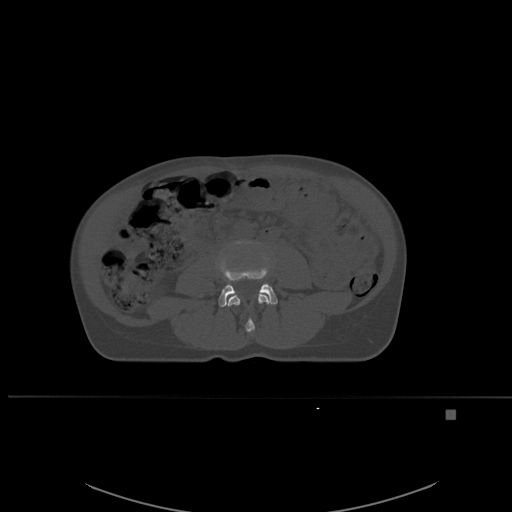
CT including the spine, one axial slice; slice 201 of 537 in the series (ordered by position); bone window (W 1800 / L 400 HU); 1.5 mm slice thickness; 512 × 512 image matrix. Female patient, age 45 years. From the clinical record (not read from this slice): primary cancer: lung.
Structures marked on this image (semi-automatically segmented with operator editing):
- L3 vertebra: bounding box [x1, y1, x2, y2] px = [227, 292, 271, 333]
- L4 vertebra: [218, 240, 278, 307]